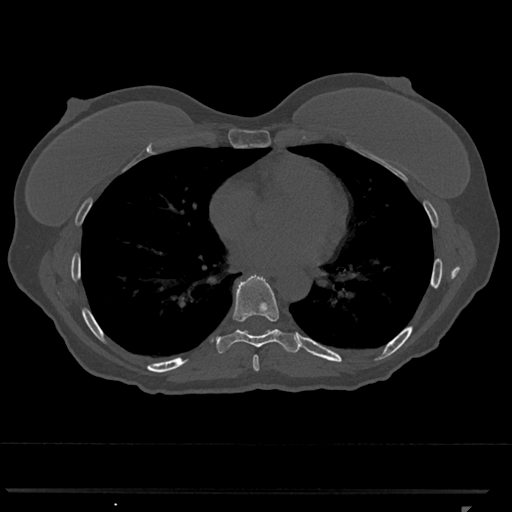
CT including the spine, one axial slice; slice 666 of 793 in the series (ordered by position); reconstruction kernel Br40s/3; 120 kVp; bone window (W 1800 / L 400 HU); 0.5 mm slice thickness; 512 × 512 image matrix. Female patient, age 62 years. From the clinical record (not read from this slice): primary cancer: renal.
Annotated regions visible in this slice (semi-automatically segmented with operator editing):
- T7 vertebra: bounding box (x1, y1, x2, y2) in pixels: (253, 355, 259, 371)
- T8 vertebra: (216, 274, 300, 354)